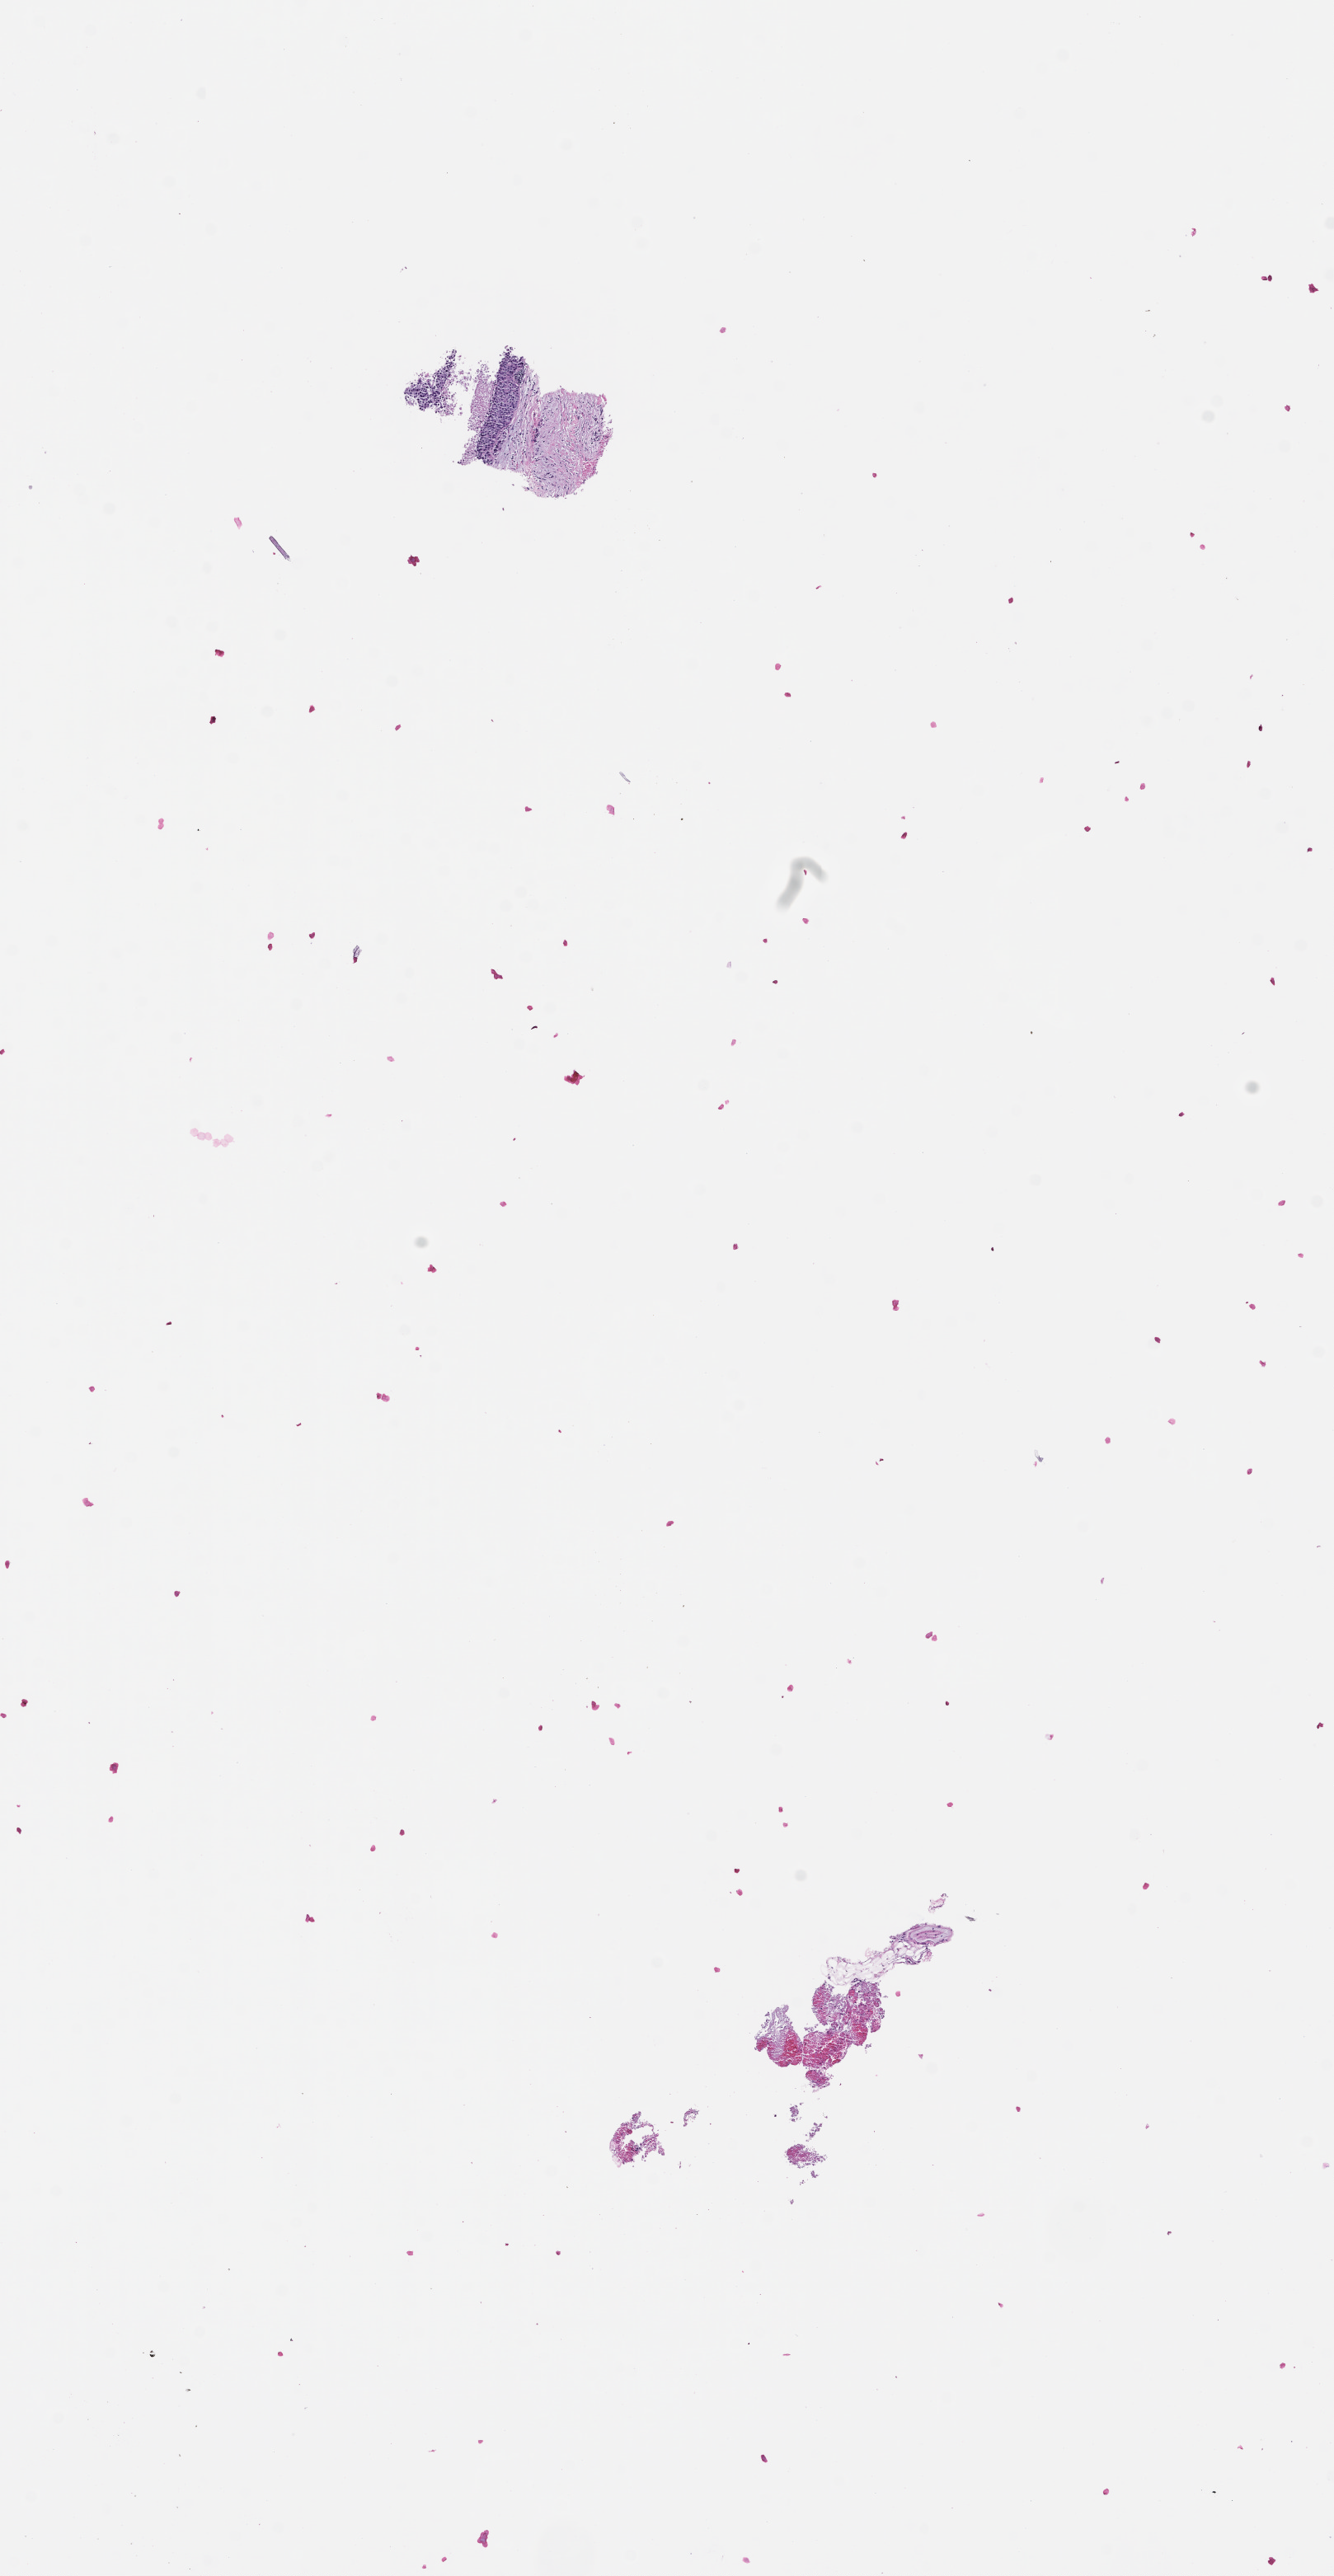
Haematoxylin and eosin whole-slide image, whole scanned area (about 6.5 x 12.6 mm) shown as a low-resolution overview, formalin-fixed, paraffin-embedded (FFPE) tissue. Patient: female.
- this section: metastatic tumor tissue
- patient diagnosis (primary): Non-Small Cell Lung Carcinoma